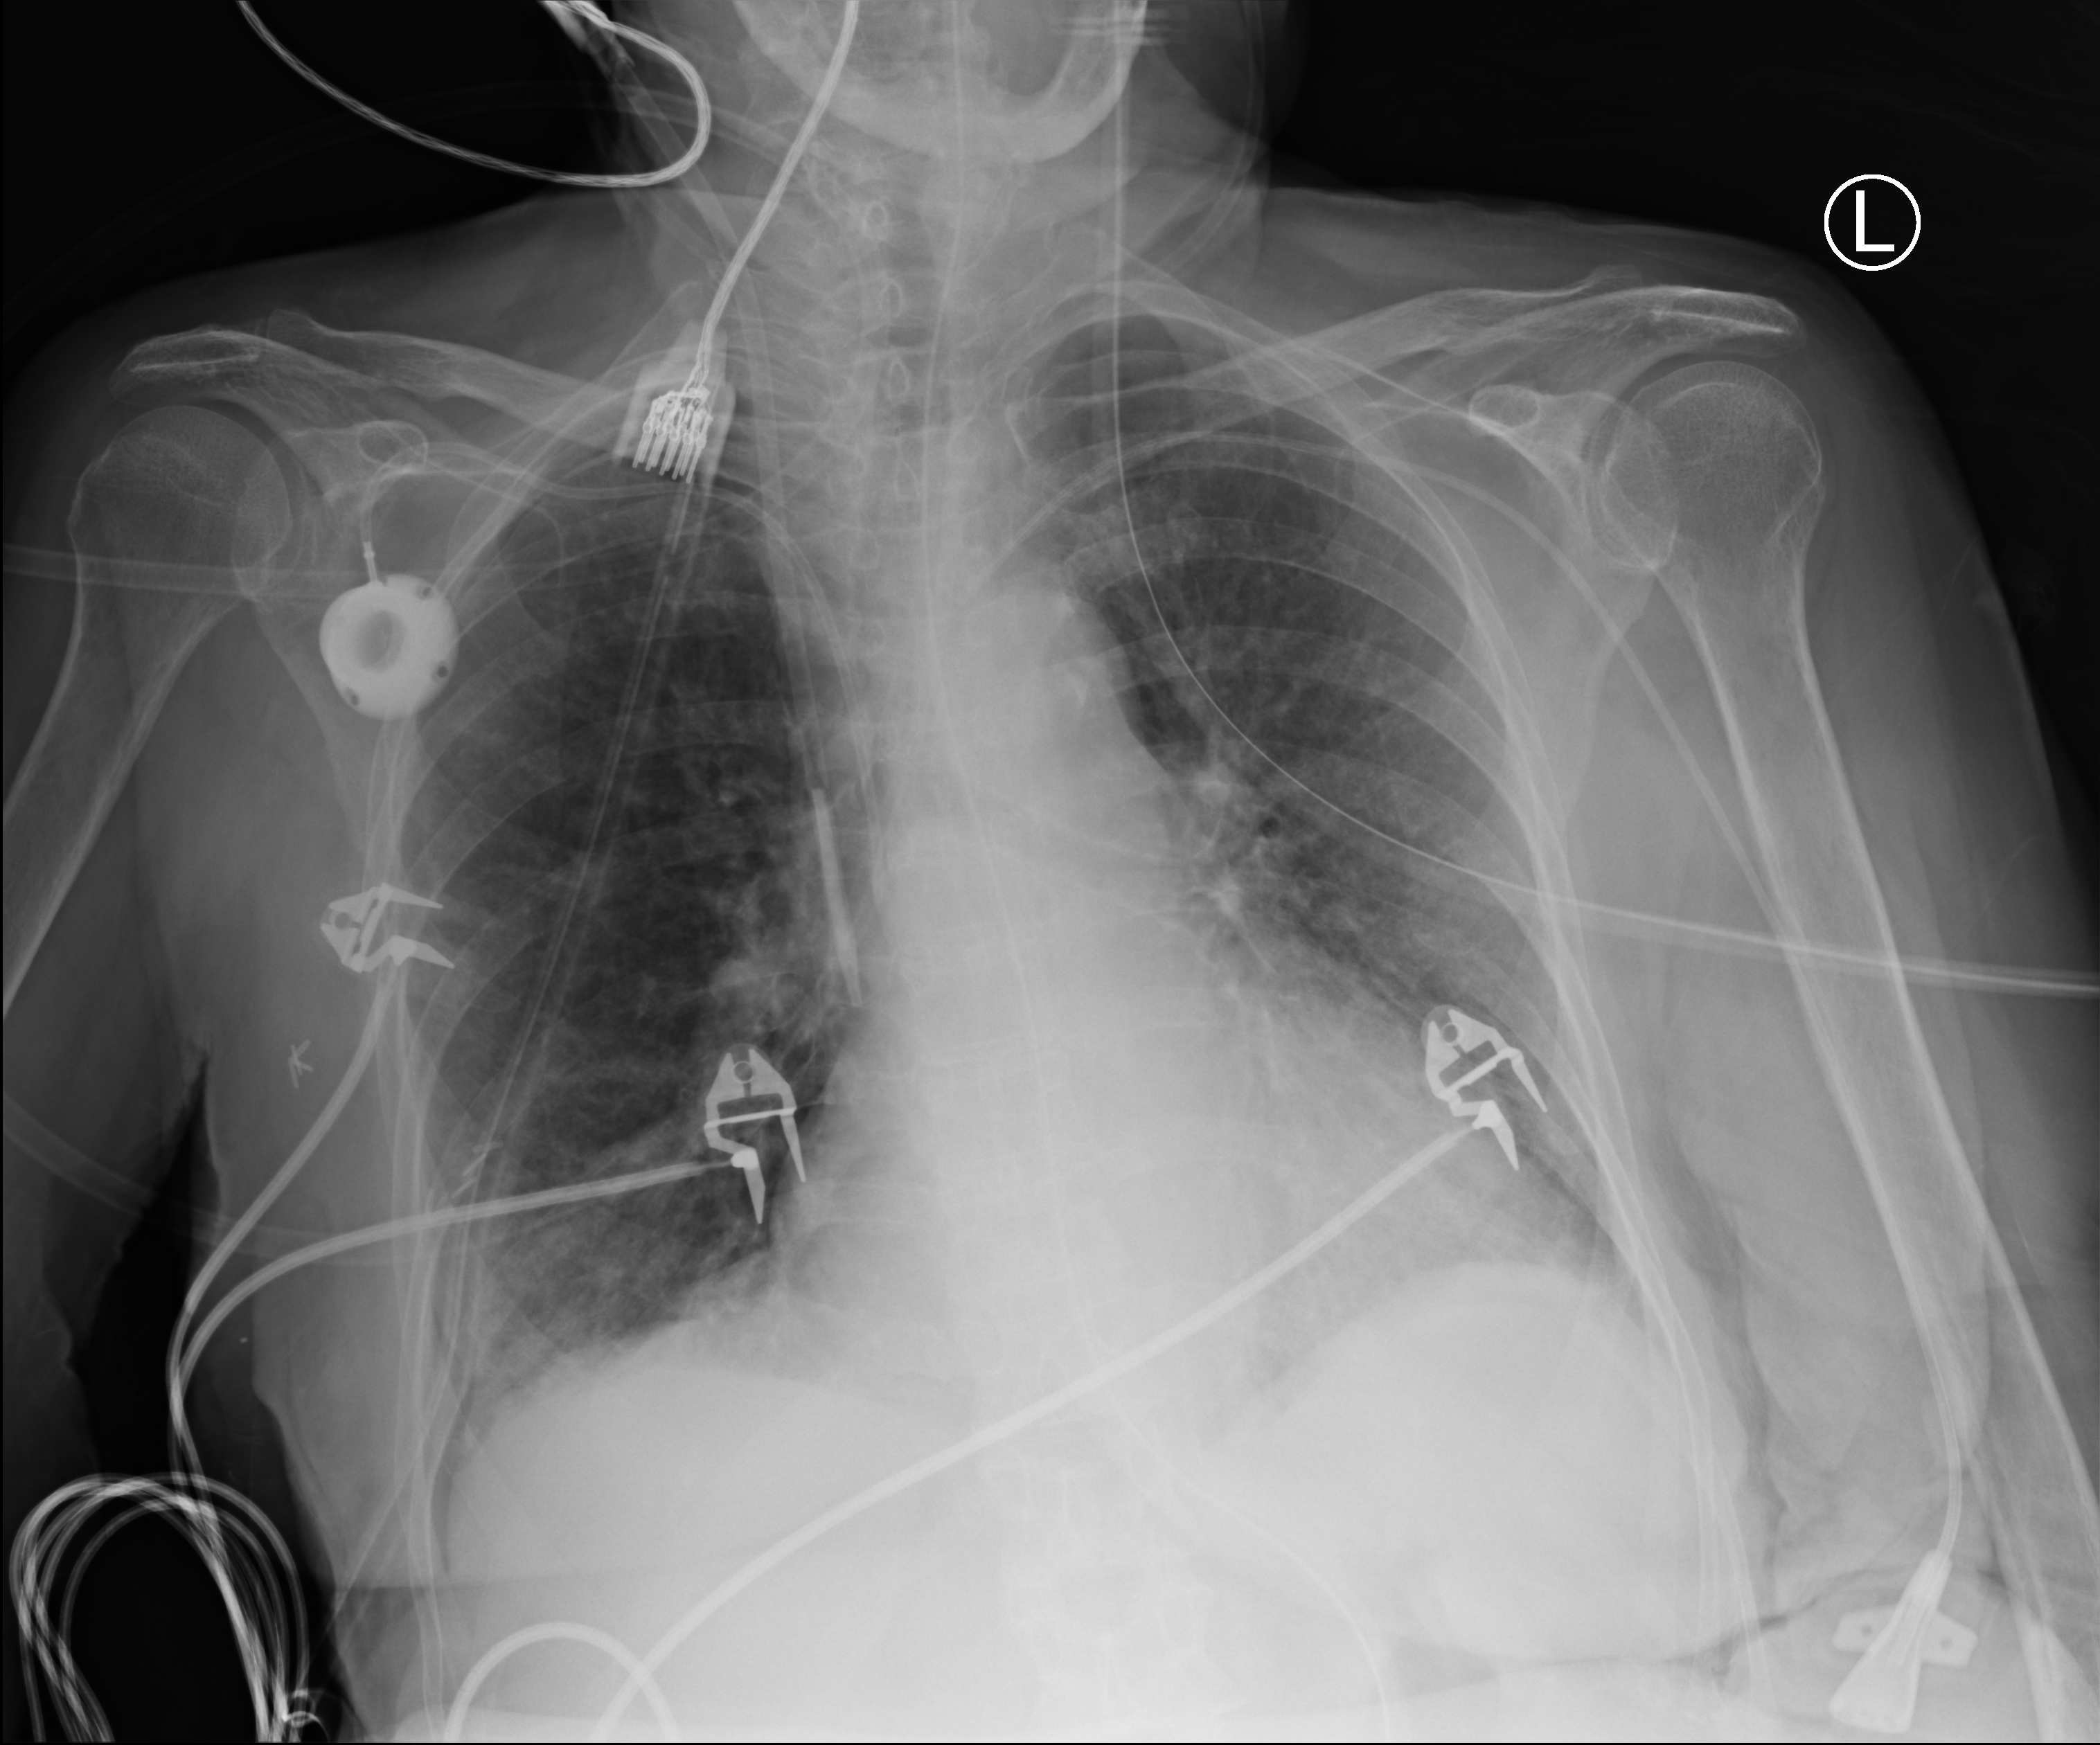
Portable chest radiograph; anteroposterior (AP) projection. Patient hospitalised with COVID-19; female, aged 60–74 years.
From the hospital-stay record, not from the radiograph (when in the stay this image was taken is not recorded): COPD (admission record): no; admitted to intensive care during this hospital stay: yes; smoking status (admission record): former.